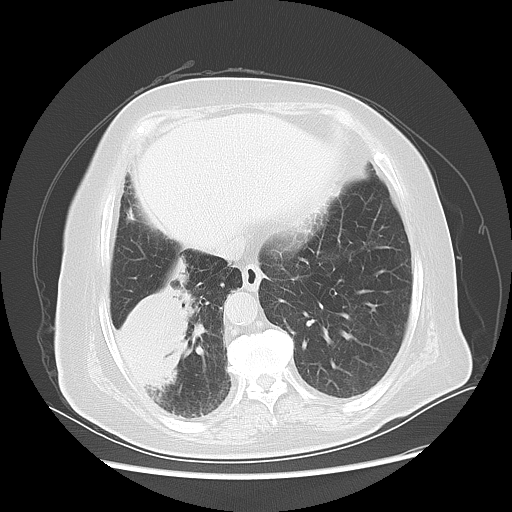
Chest CT, one axial slice. Slice 17 of 56 in the series (ordered by position). 120 kVp. Lung window (W 1500 / L -600 HU). 5 mm slice thickness. 512 × 512 image matrix, field of view 378 × 378 mm. Female patient, age 73 years. Case-level facts recorded for this patient, not image findings: clinical TNM (as recorded): T3 N0 M0.
Structures marked on this image (rectangle marked by the reading radiologist):
- lung tumour (recorded histology: adenocarcinoma): bounding box [x1, y1, x2, y2] px = [108, 255, 197, 392]